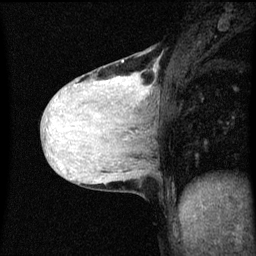
Breast MRI (dynamic contrast-enhanced), one sagittal slice. Position 26 of 60 along the scan axis. Dynamic contrast-enhanced series, image 2 of 3 at this slice position (ordered by acquisition). 1.5 T. TE 4.2 ms, TR 8.4 ms. 2 mm slice thickness. 256 × 256 image matrix. Patient: female, 36 years.
Annotated regions visible in this slice (semi-automatic segmentation, software-assisted and operator-edited):
- analysis volume of interest (the breast-tissue region the enhancement analysis was run in; not a lesion): bounding box (x1, y1, x2, y2) in pixels: (48, 52, 157, 151)
- tumour enhancement mask (voxels above the 70 % enhancement threshold inside the analysis volume of interest): (142, 92, 147, 95)